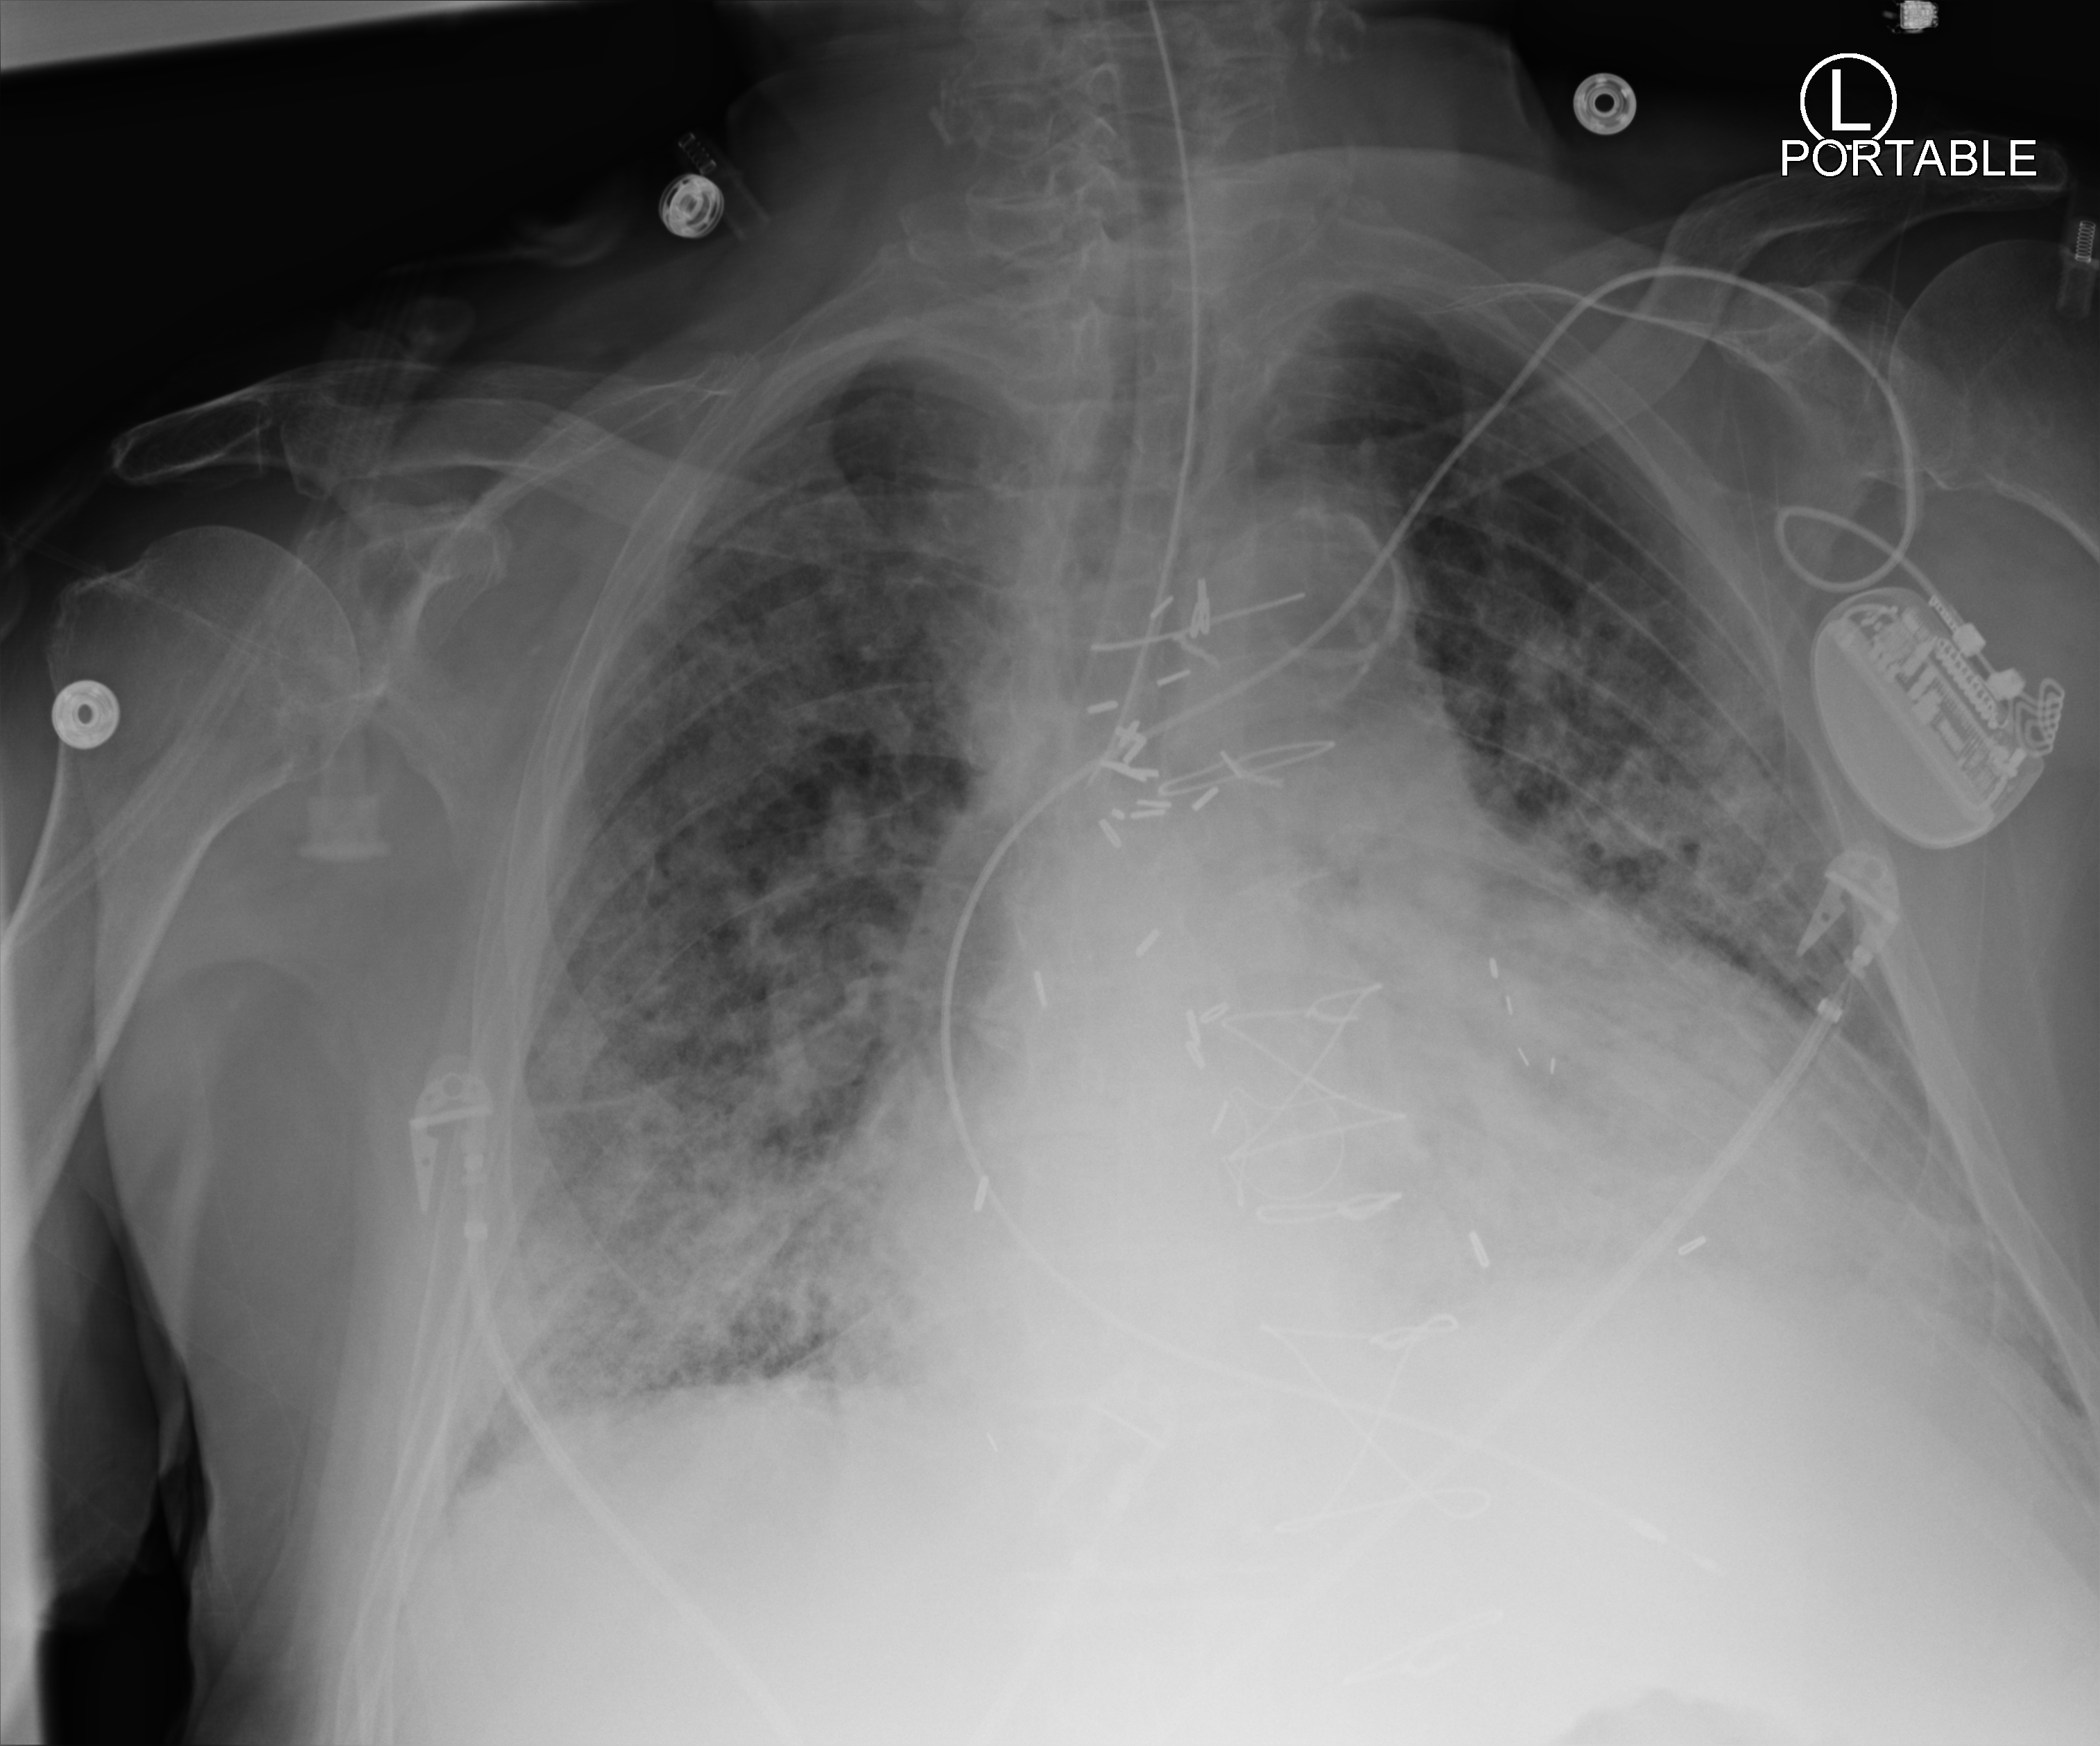
Chest X-ray (portable); anteroposterior (AP) projection. Patient hospitalised with COVID-19; male, aged 75–90 years.
Admission-level facts for this patient (not findings on this image; timing relative to this image not recorded):
- smoking status (admission record): former
- diabetes (admission record): yes
- admitted to intensive care during this hospital stay: yes